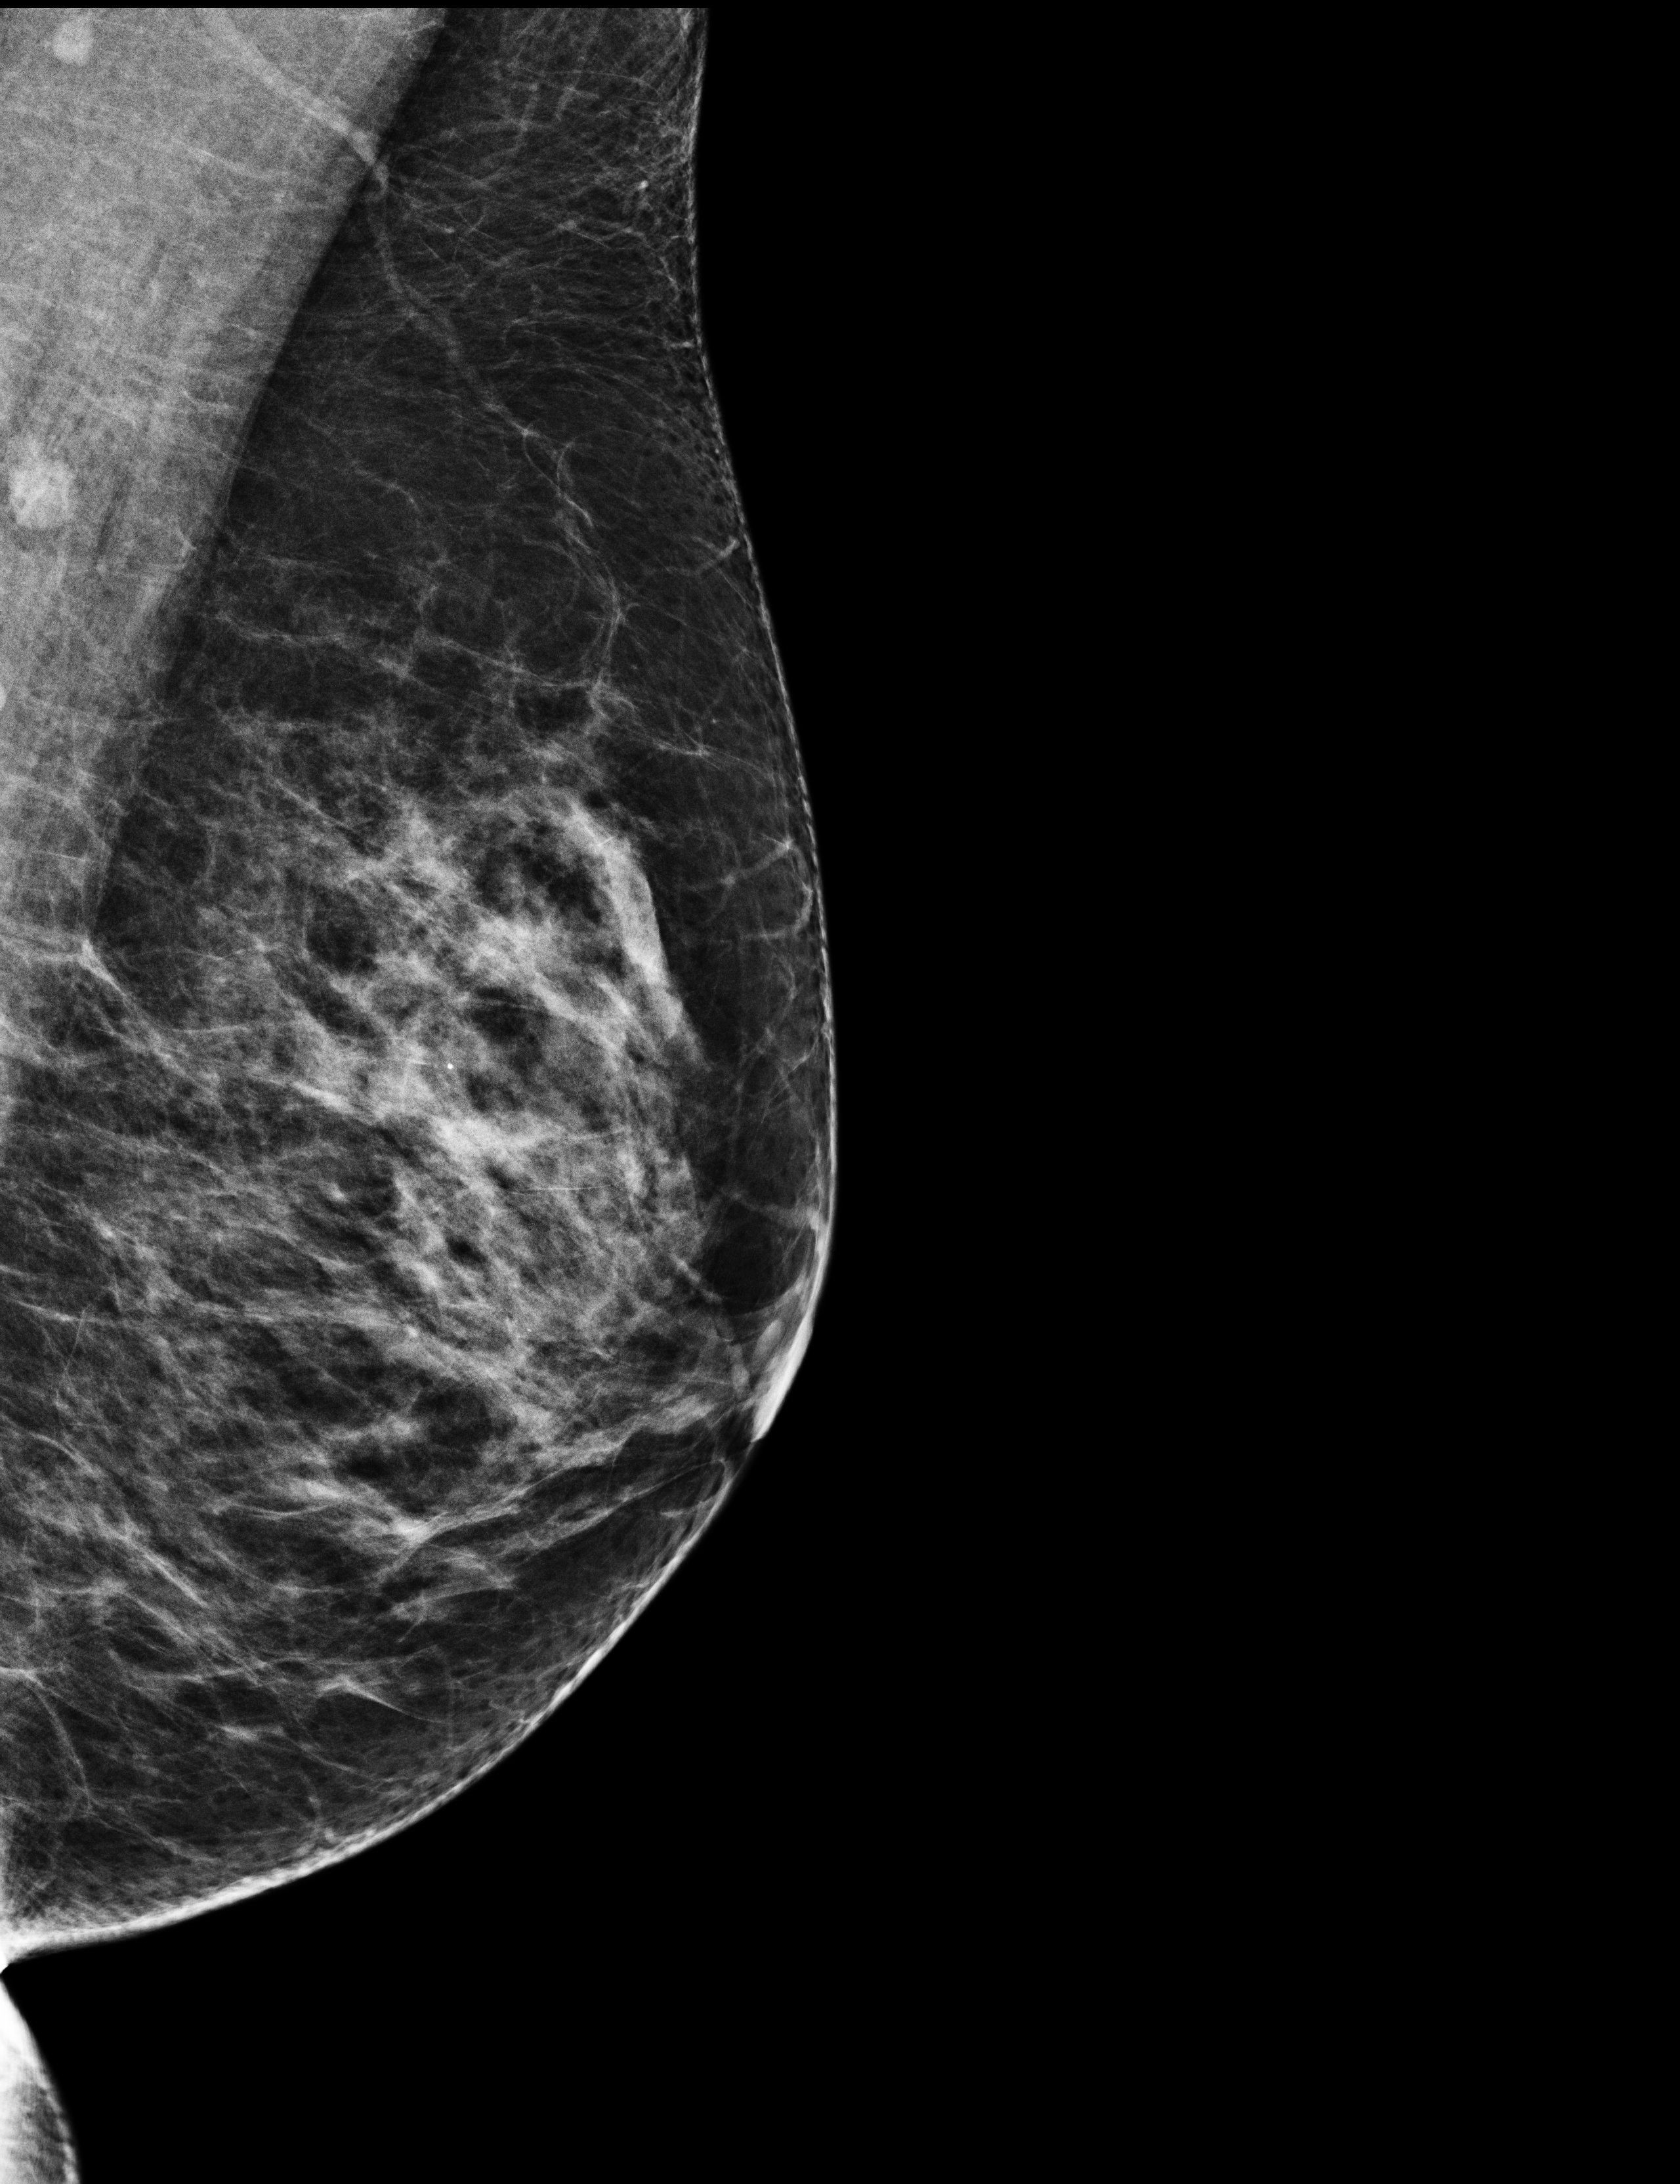
Annual screening mammography examination; system: Selenia Dimensions. Patient: female, 55 years.
Image type: full-field digital mammogram. Breast: left. Projection: mediolateral oblique (MLO) view.